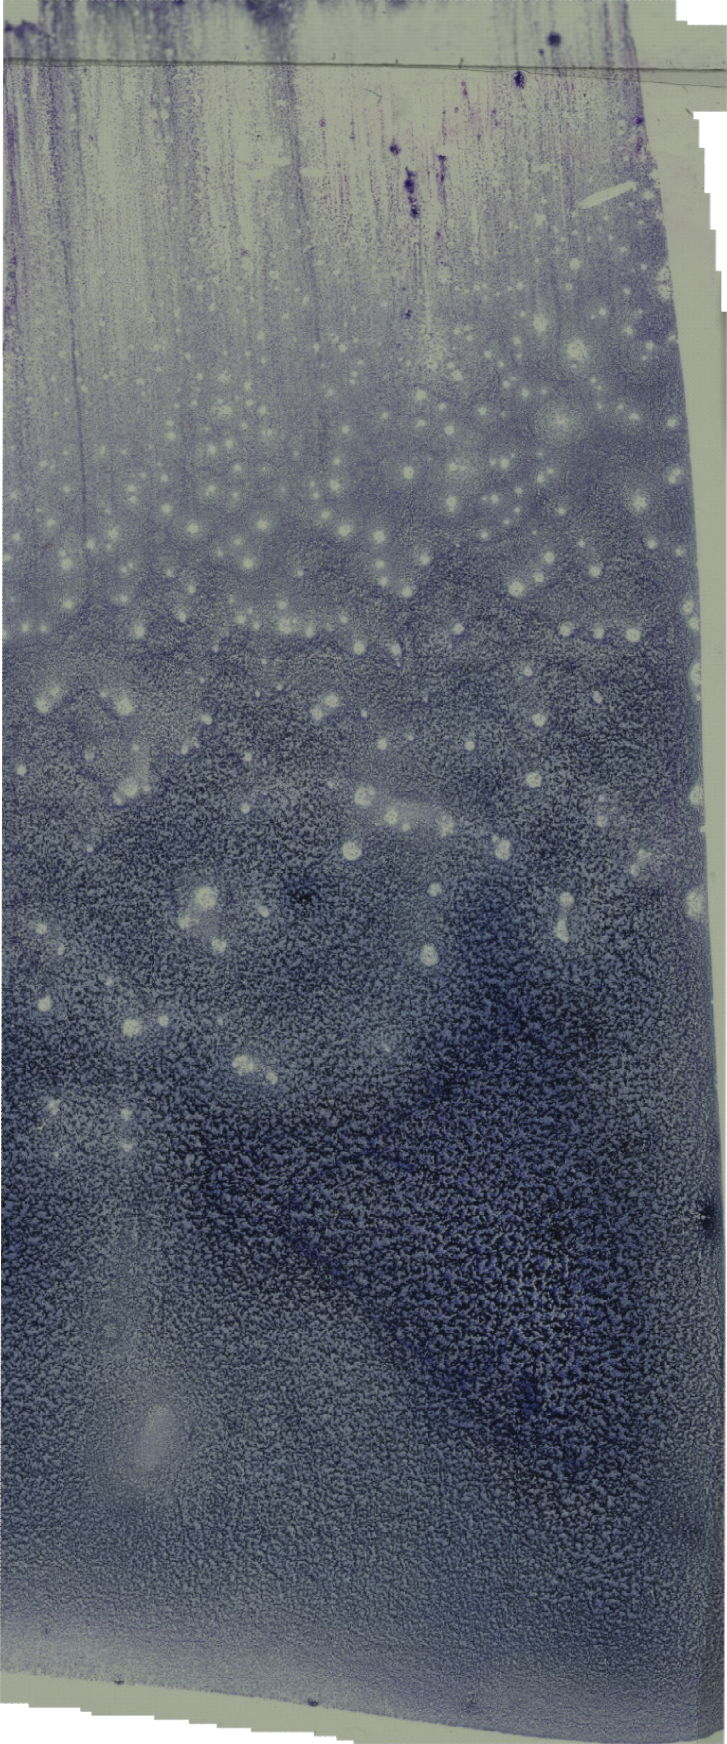
May-Grünwald–Giemsa-stained marrow aspirate smear (whole slide), a low-resolution overview of the entire scanned area, about 20.6 x 49.4 mm. Patient sex: female.
Diagnosis: Acute Myeloid Leukemia without Maturation.